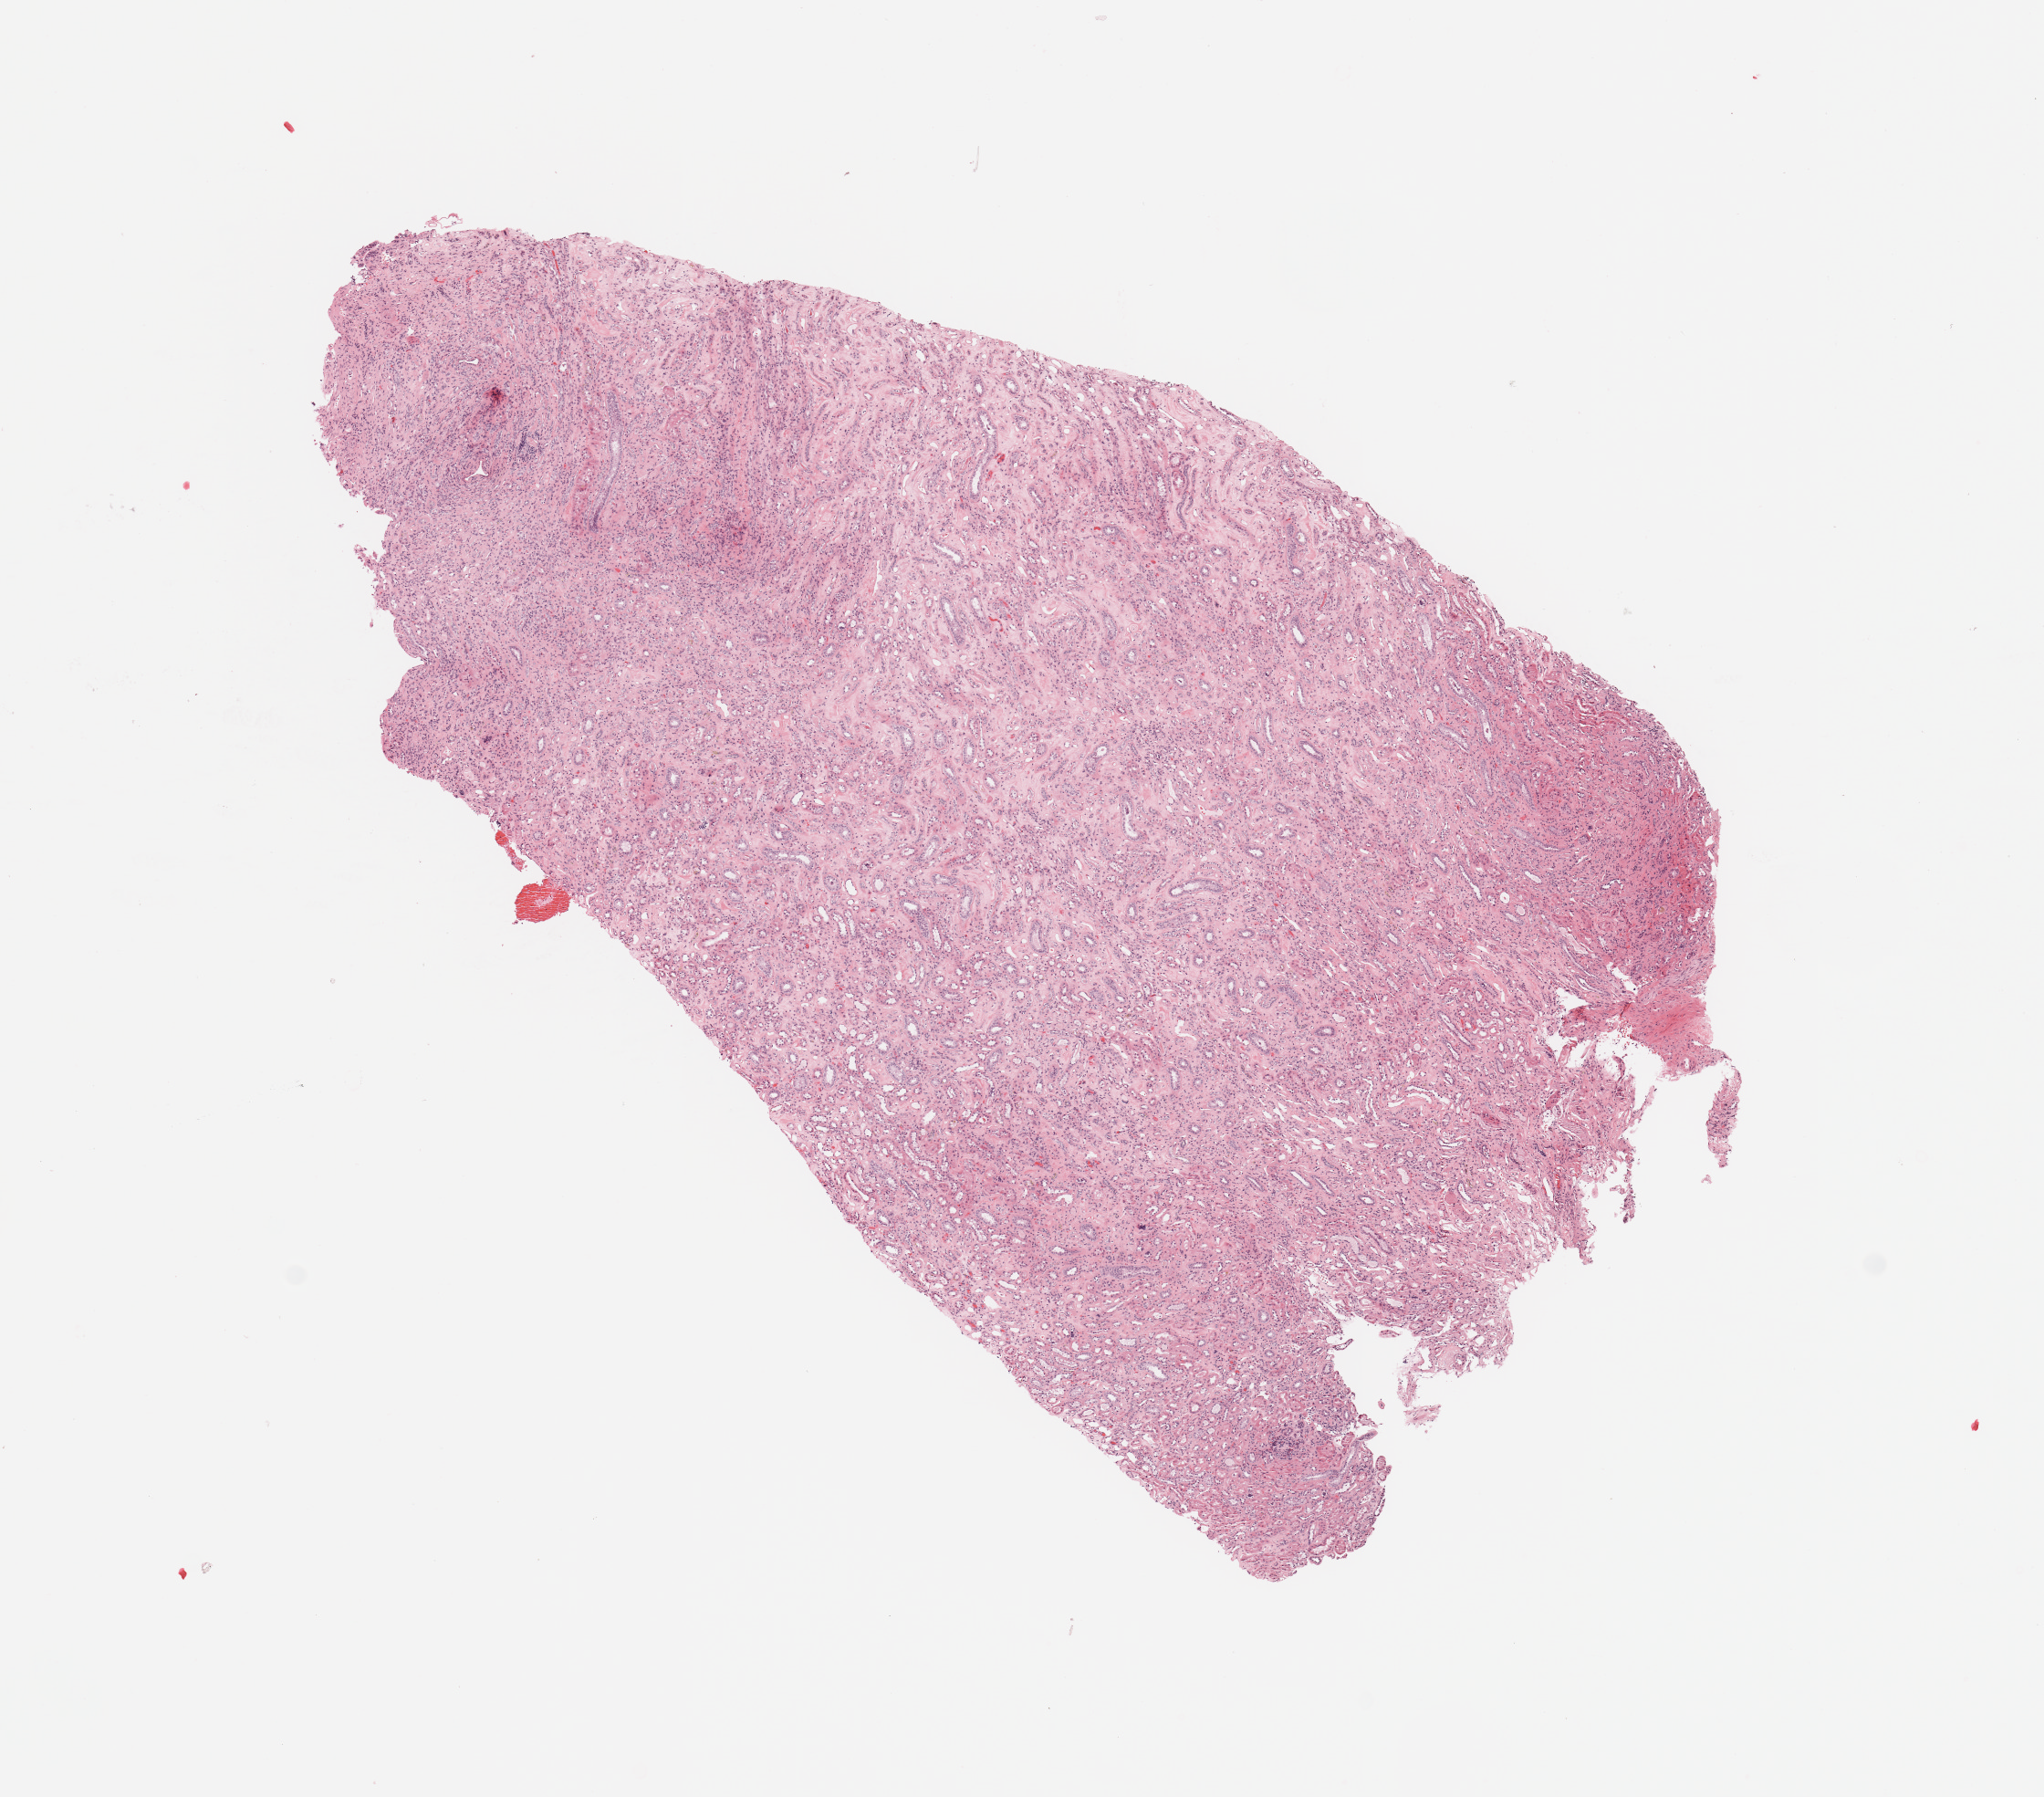
Whole-slide histology image, Hematoxylin and eosin (H&E) stained — a low-resolution overview of the entire scanned area, about 8.9 x 7.8 mm (acquisition: 20x scan). Normal (non-tumour) tissue sample, kidney. 89-year-old female patient.
- this section: normal (non-tumour) tissue from the same patient
- patient diagnosis: Renal cell carcinoma, NOS